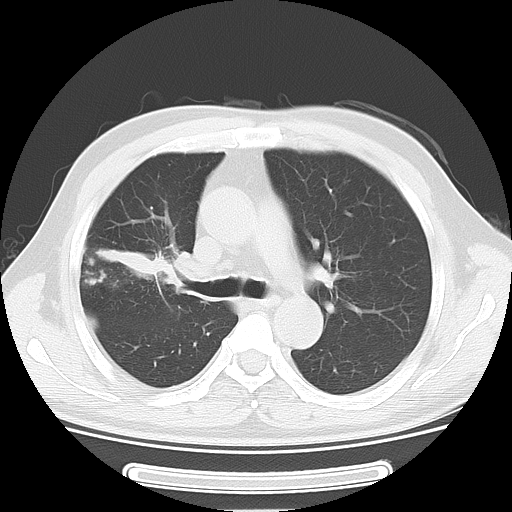
Chest CT, one axial slice. Slice 34 of 51 in the series (ordered by position). Reconstruction kernel LUNG. Lung window (W 1500 / L -600 HU). 512 × 512 image matrix. Male patient, age 46 years. From the clinical record (not read from this slice): clinical TNM (as recorded): T3 N0 M1b.
Structures marked on this image (rectangle marked by the reading radiologist):
- lung tumour (recorded histology: adenocarcinoma): bounding box (x1, y1, x2, y2) in pixels: (92, 230, 190, 298)